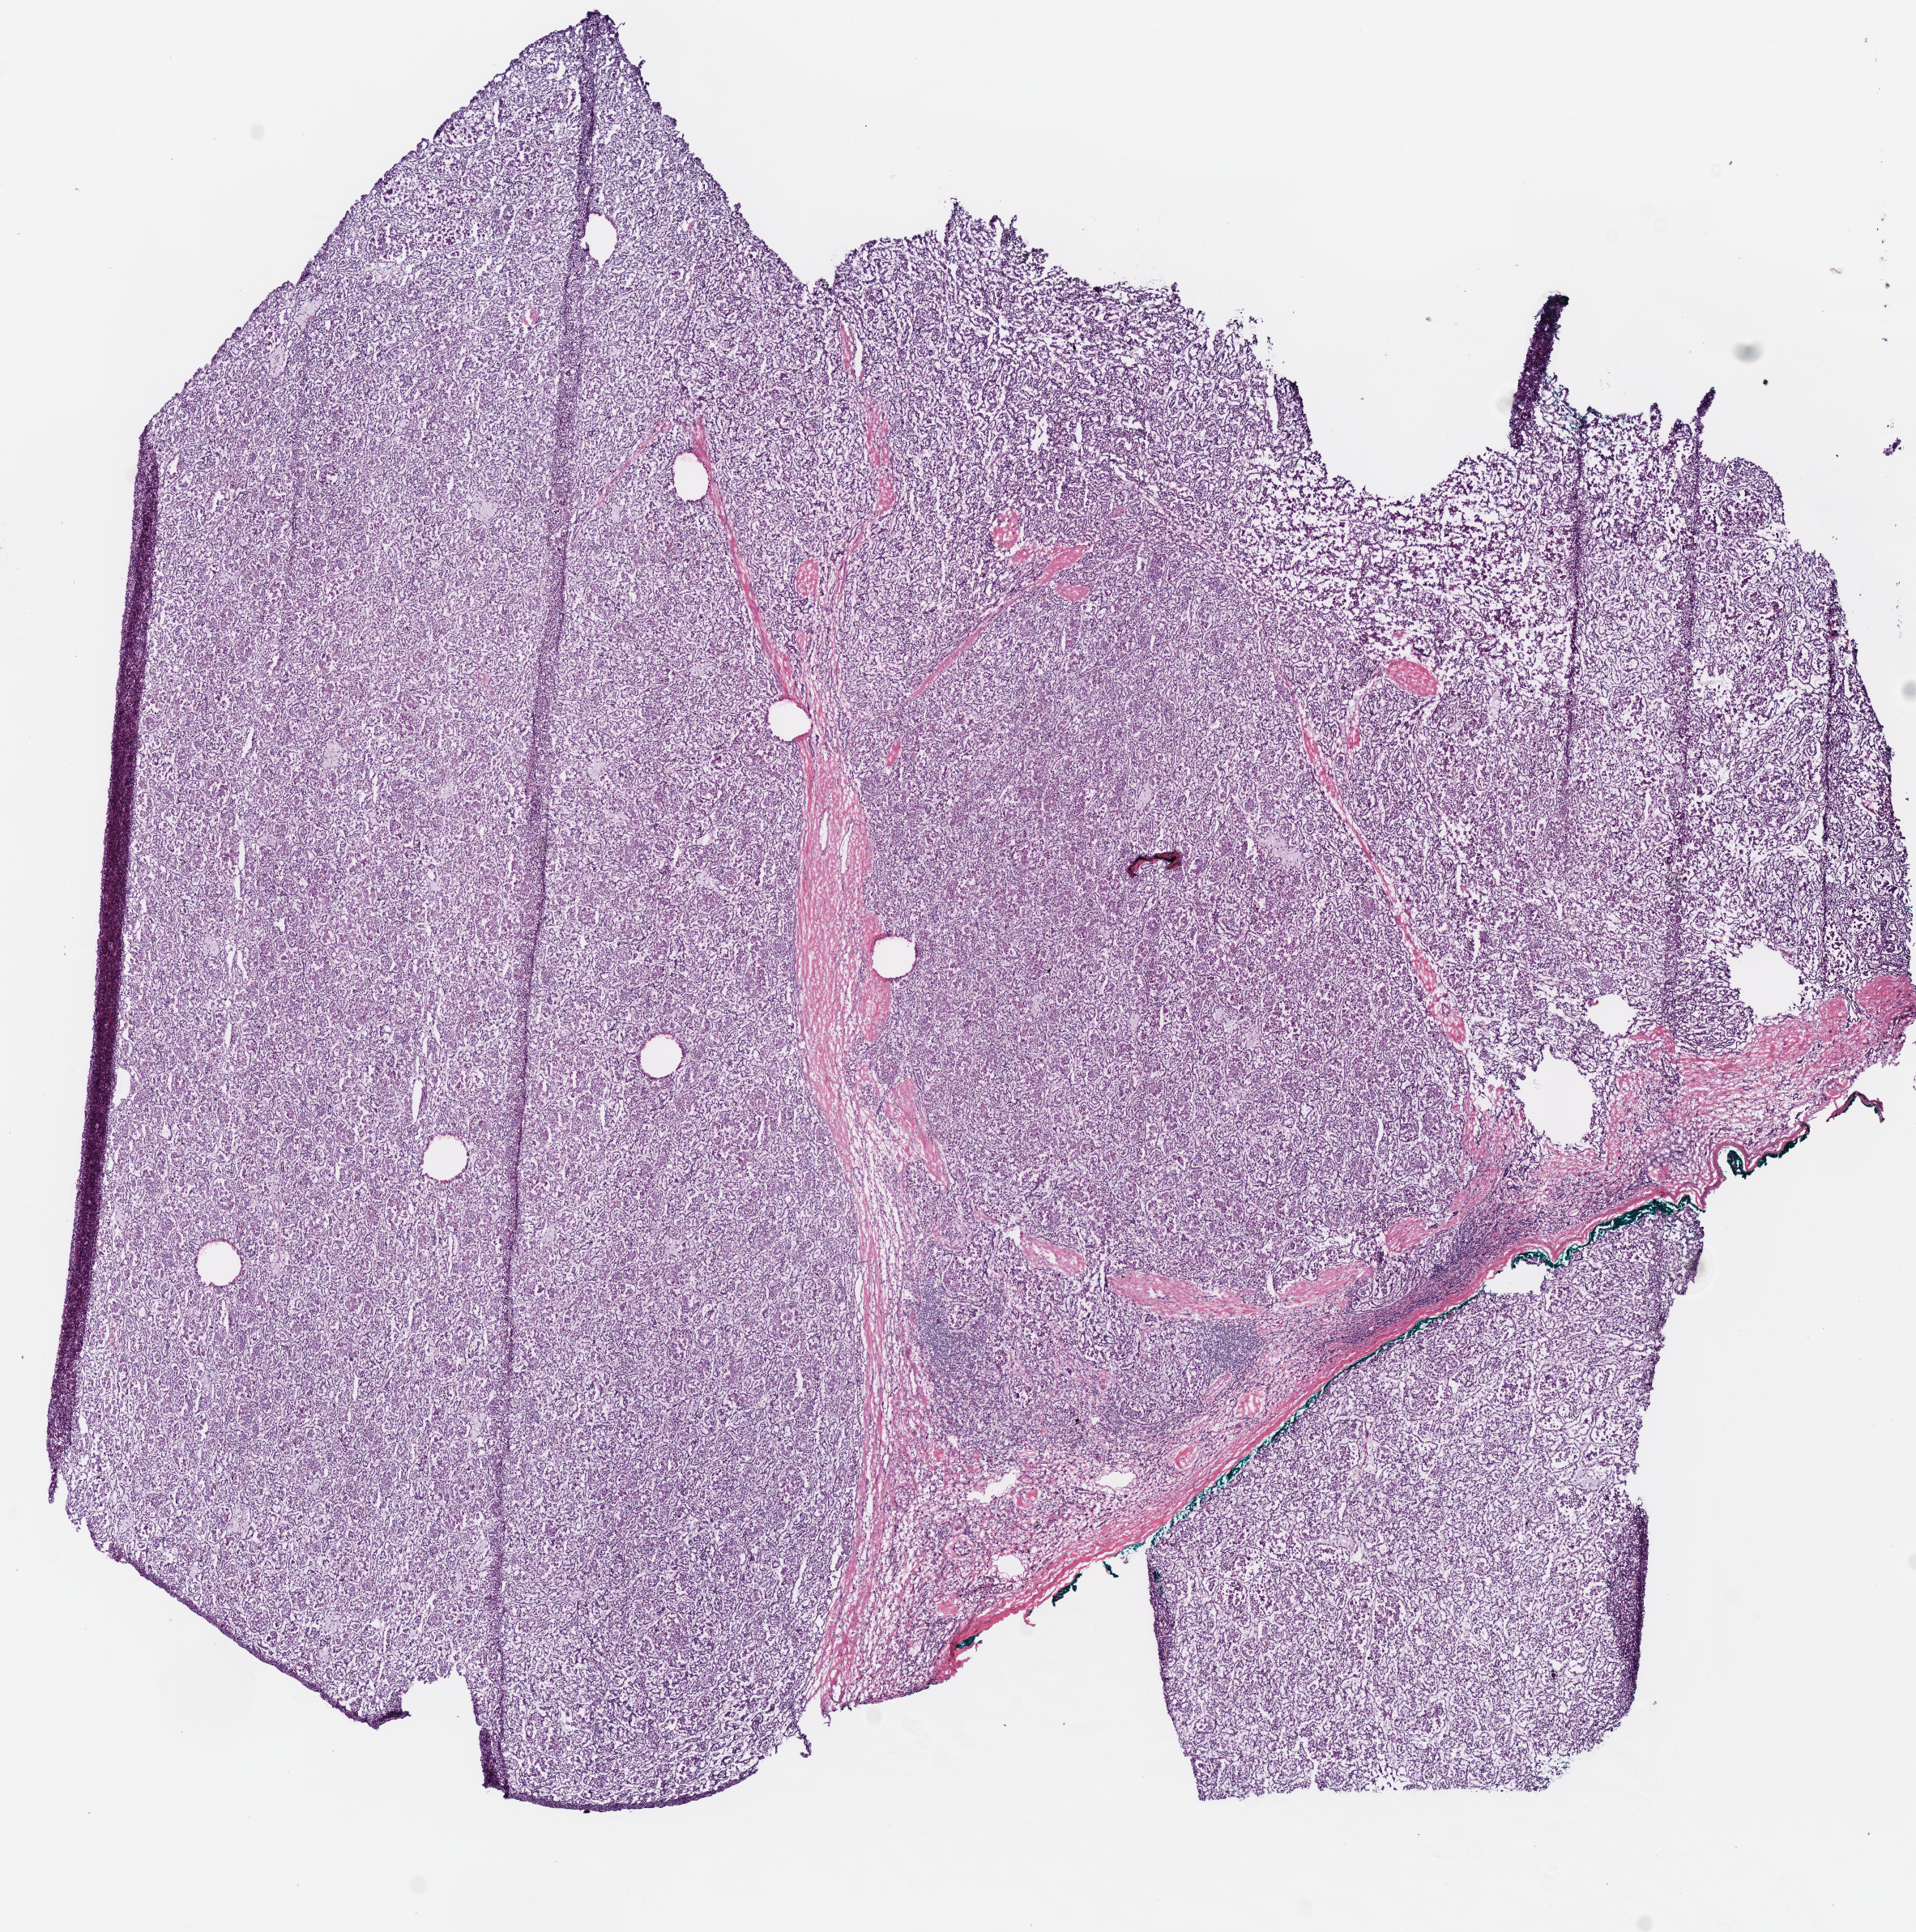
Digitized Hematoxylin and eosin (H&E) stained tissue section (whole slide), whole scanned area (about 9.3 x 9.4 mm) shown as a low-resolution overview. Frozen section from the bottom of the tissue portion. Sample: primary tumour, kidney. Female, age 53 years at initial diagnosis. Slide review estimates, as recorded: tumour cells 90%, tumour nuclei 50%, normal cells 0%, stromal cells 10%, necrosis 0%.
Laterality: right. AJCC pathologic stage: I. Diagnosis: Papillary adenocarcinoma, NOS.